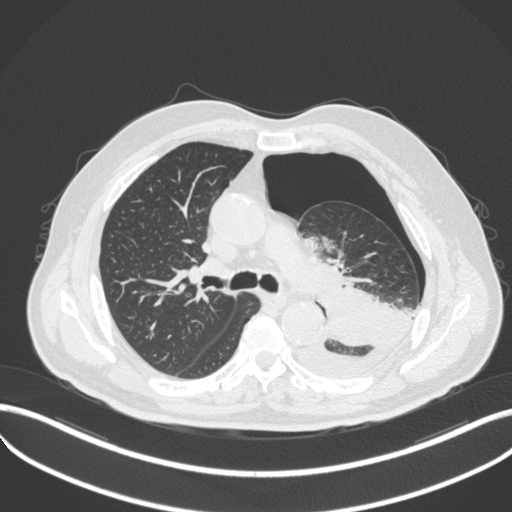
Chest CT, one axial slice; reconstruction kernel B31f; 120 kVp; lung window (W 1500 / L -600 HU); 1 mm slice thickness; 512 × 512 image matrix. Patient: male, 76 years. Case-level facts recorded for this patient, not image findings: clinical TNM (as recorded): T3 N0 M1b.
Annotated regions visible in this slice (bounding box drawn by a radiologist):
- lung tumour (recorded histology: adenocarcinoma): bounding box [x1, y1, x2, y2] px = [308, 282, 388, 350]